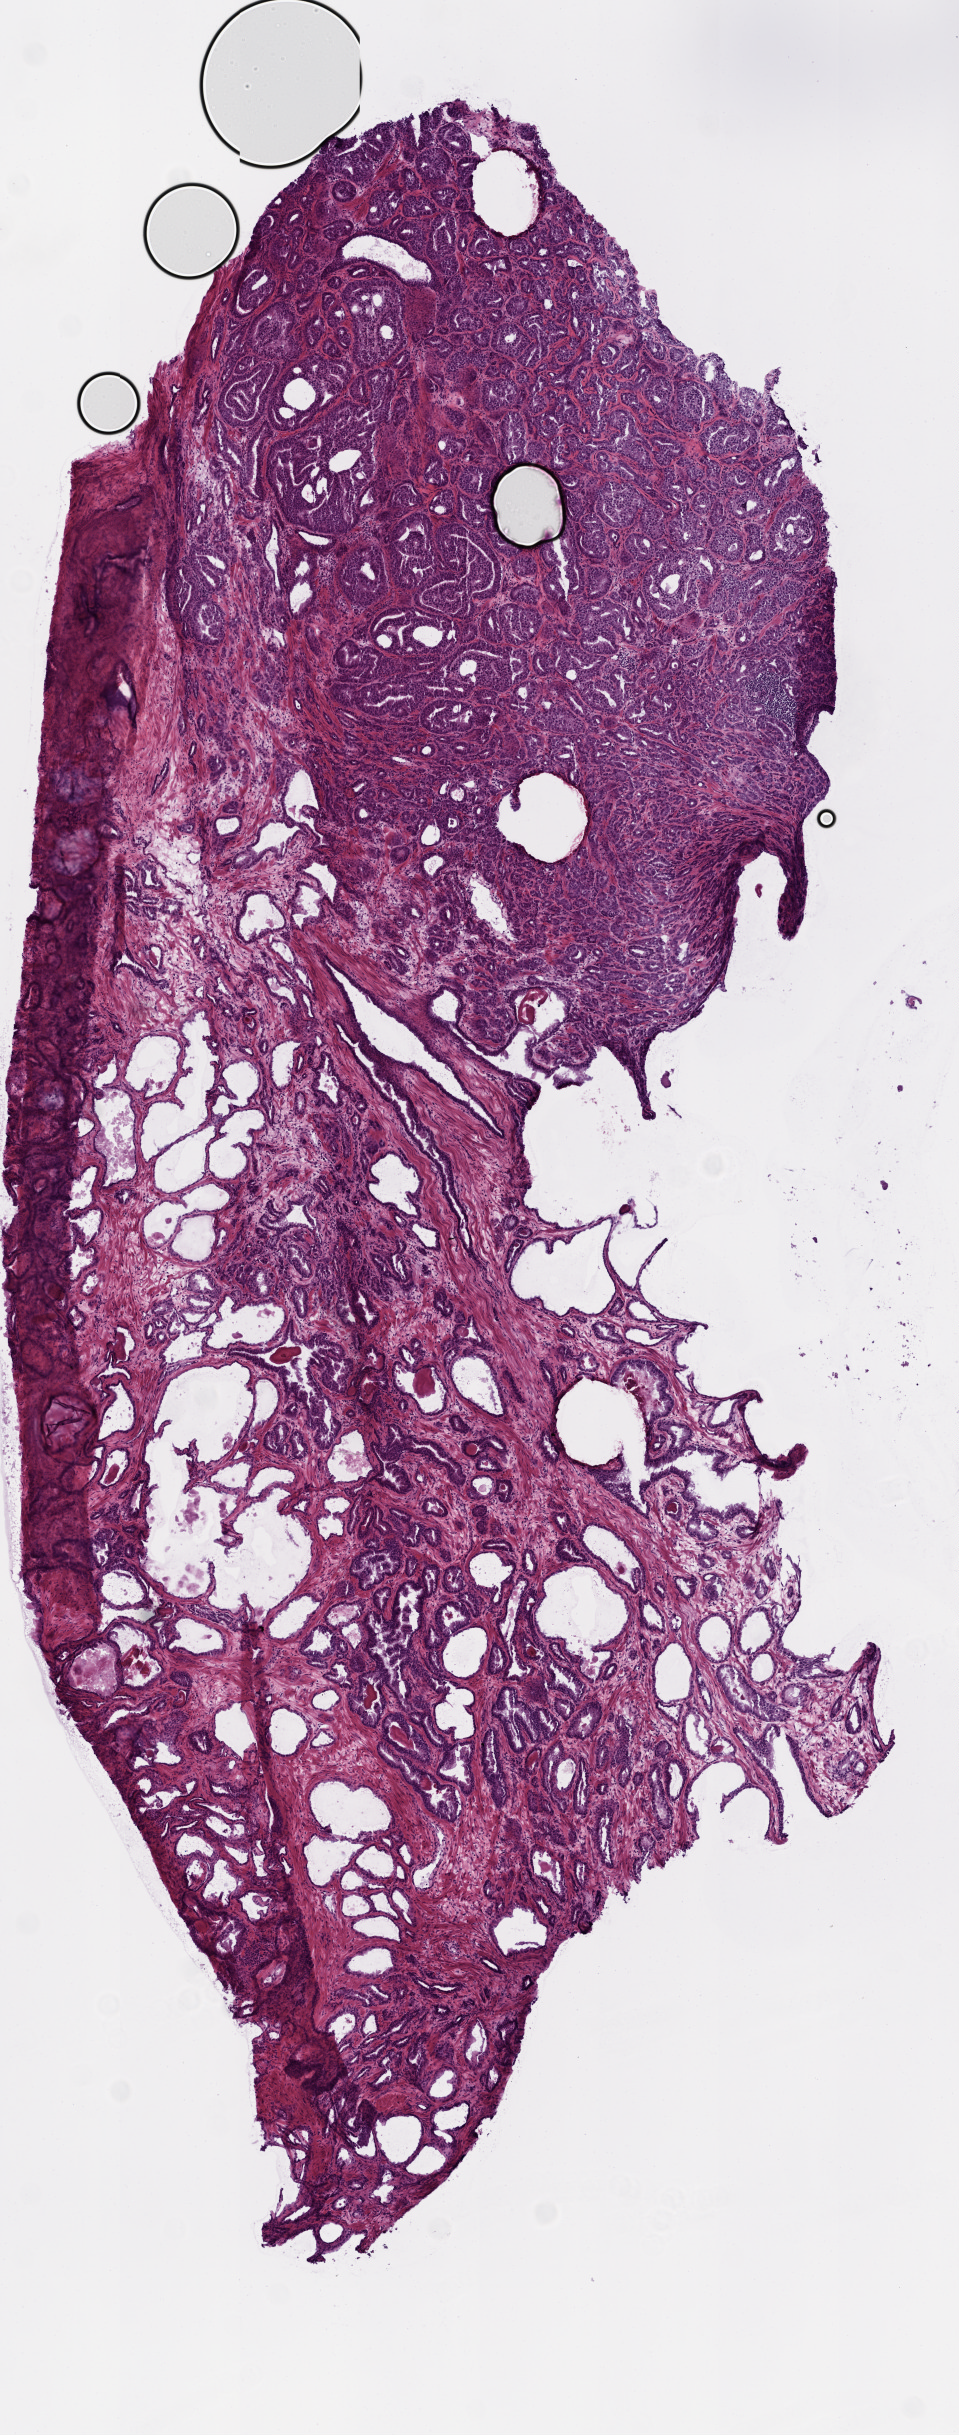
Digitized H&E-stained tissue section (whole slide), shown as a low-resolution overview of the whole scanned area (about 3.9 x 9.8 mm, slide scanned at 20x). Frozen section from the top of the tissue portion. Prostate, primary tumour sample. Male patient; age at initial diagnosis 53 years. Gleason score: 7 (3+4). Composition of this section per pathologist review: tumour cells 85%, tumour nuclei 85%, normal cells 10%, stromal cells 5%, necrosis 0%.
- diagnosis: Acinar cell carcinoma (prostate gland)